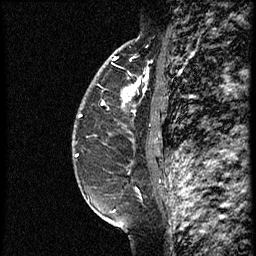
Breast MRI (dynamic contrast-enhanced), one sagittal slice. Slice 43 of 60 in the series (ordered by position). Dynamic contrast-enhanced study with each time point stored as its own series, time point 2 of 3 at this slice position (early post-contrast, ordered by acquisition time). 1.5 T. TE 4.2 ms, TR 18.9 ms. 2 mm slice thickness. 256 × 256 image matrix, field of view 200 × 200 mm. Female patient. Case-level facts recorded for this patient, not image findings: setting: breast cancer imaged before/during neoadjuvant chemotherapy; receptor status: HER2-positive.
Structures marked on this image (semi-automatic segmentation, software-assisted and operator-edited):
- analysis volume of interest (the breast-tissue region the enhancement analysis was run in; not a lesion): bounding box <77,64,161,147> (left, top, right, bottom; pixels)
- tumour enhancement mask (voxels above the 100 % enhancement threshold inside the analysis volume of interest): <104,71,149,114>